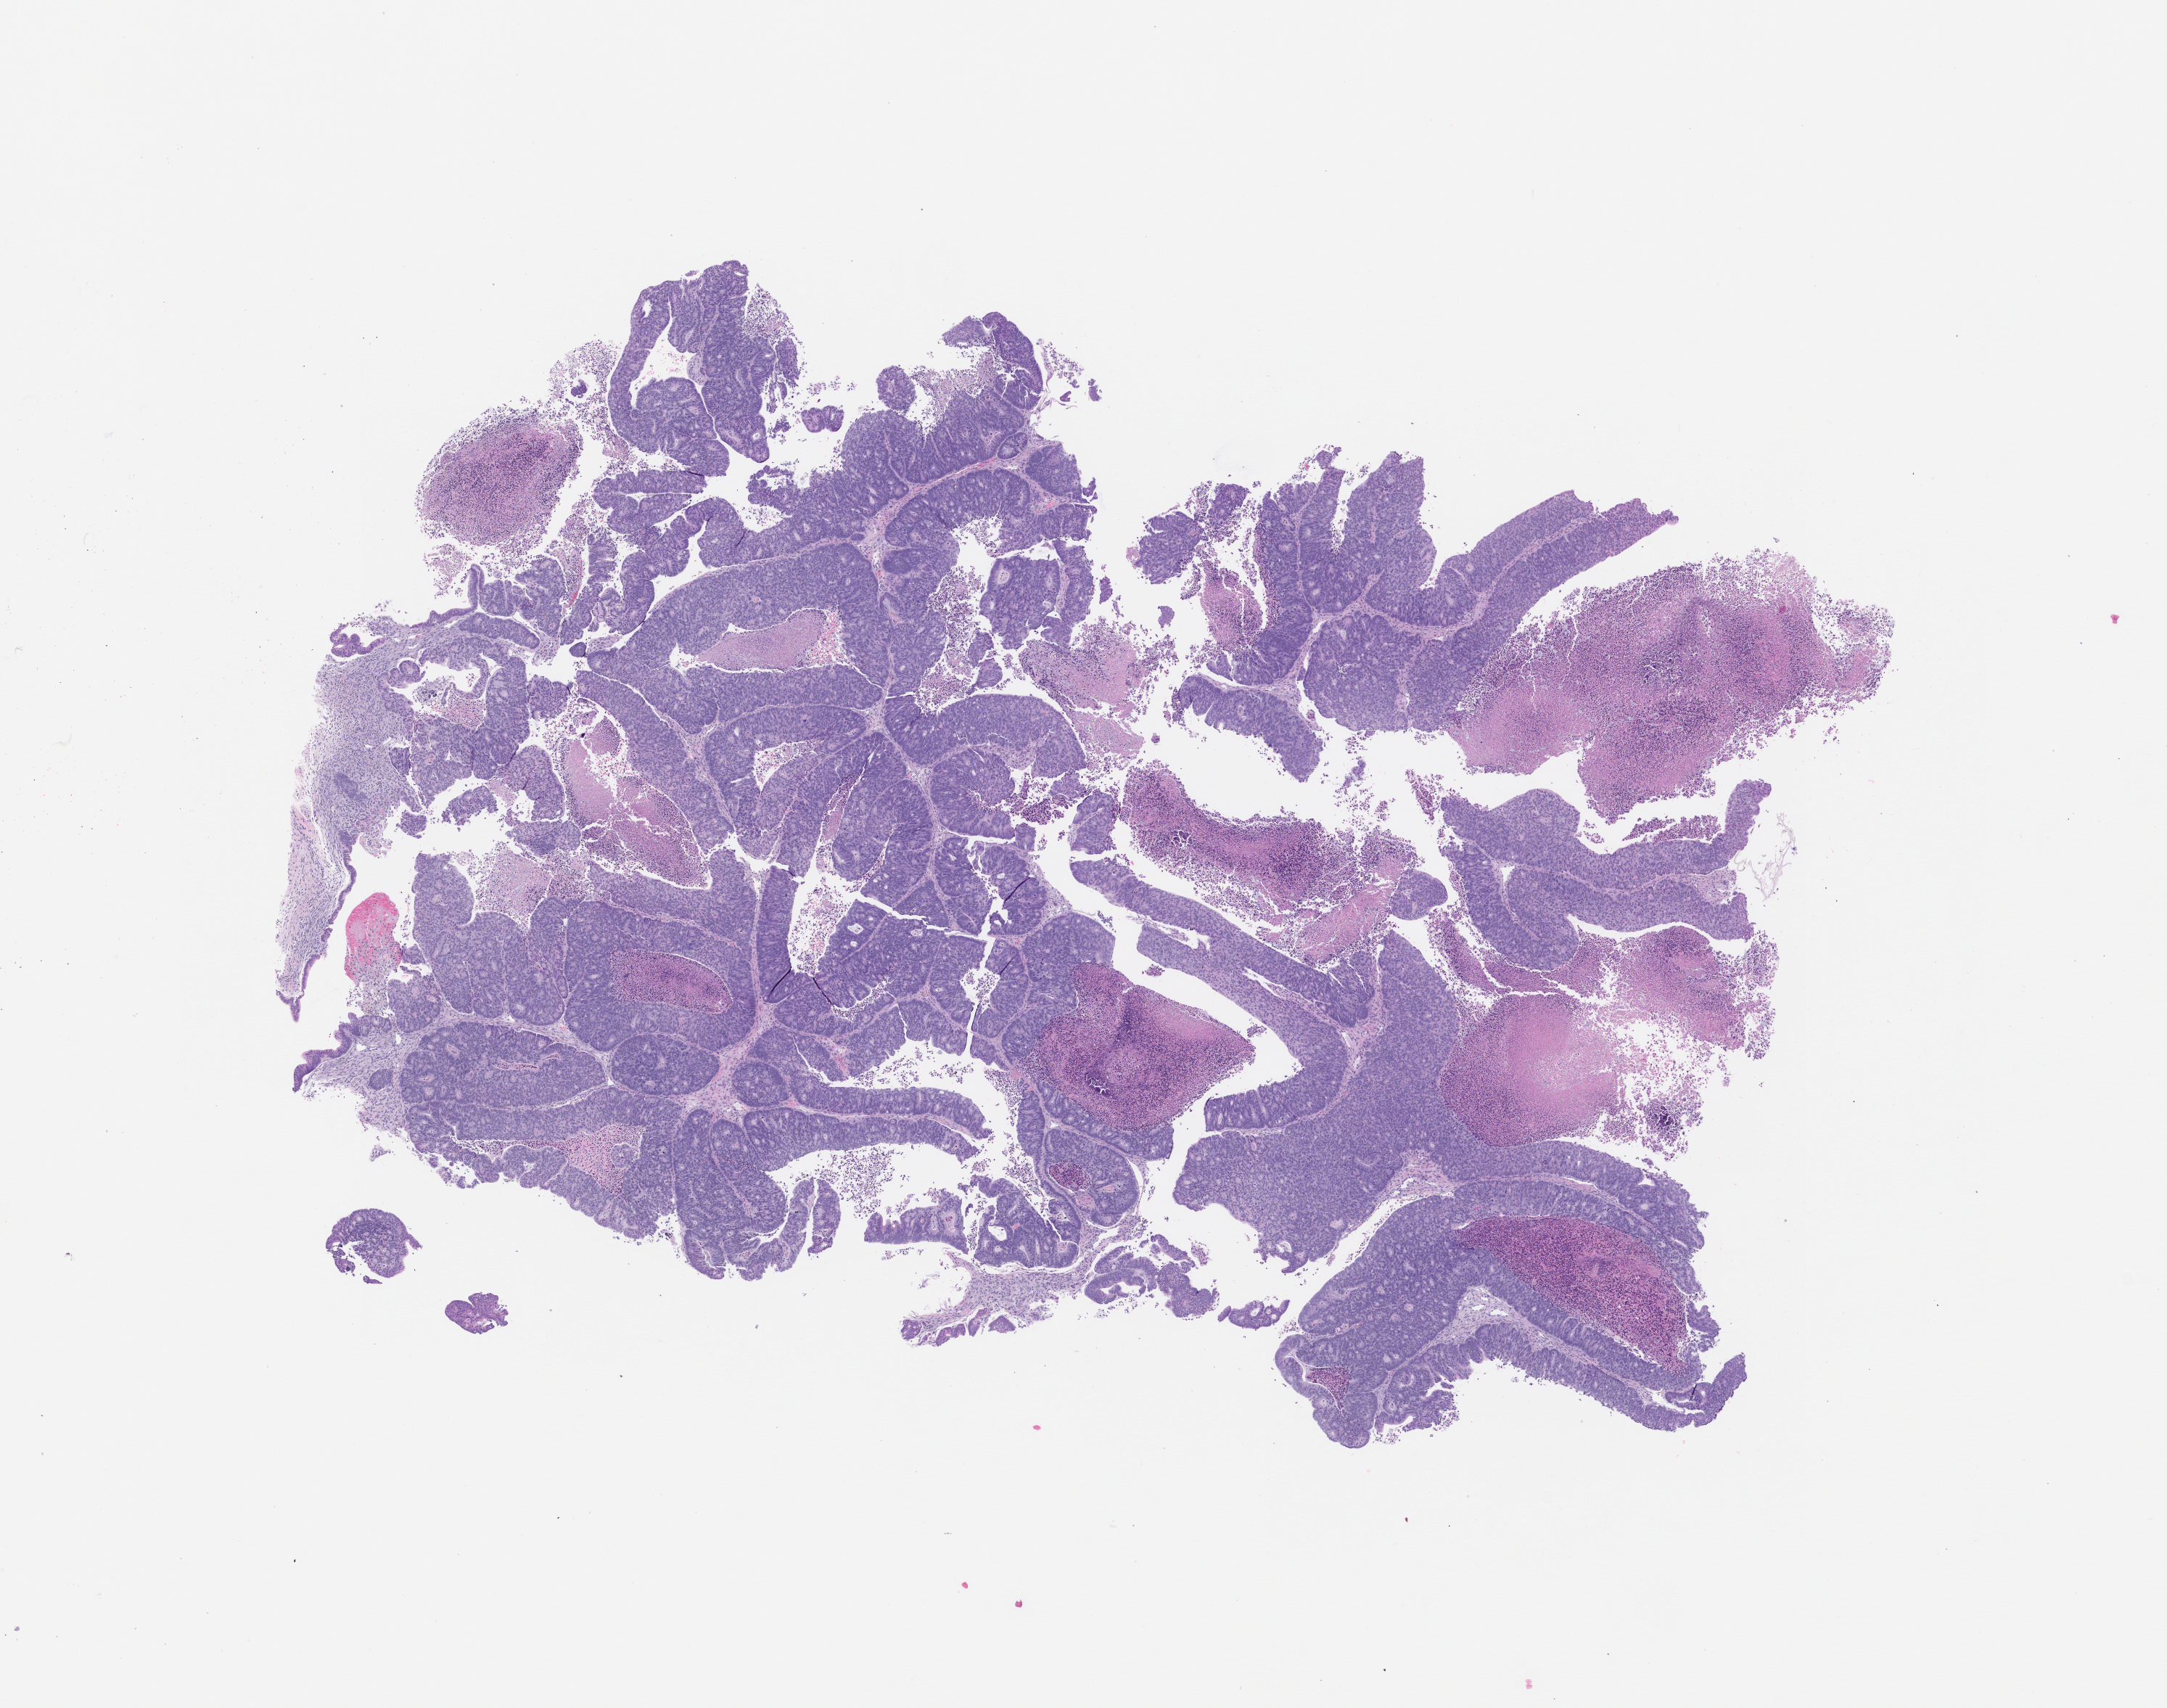
Hematoxylin and eosin (H&E) whole-slide image of a patient-derived xenograft (PDX) tumor grown in a mouse, passage 1, a low-resolution overview of the entire scanned area, about 12.0 x 9.4 mm, formalin-fixed, paraffin-embedded (FFPE) tissue, originating tumor site category: colon.
* originating patient diagnosis: Colon Adenocarcinoma